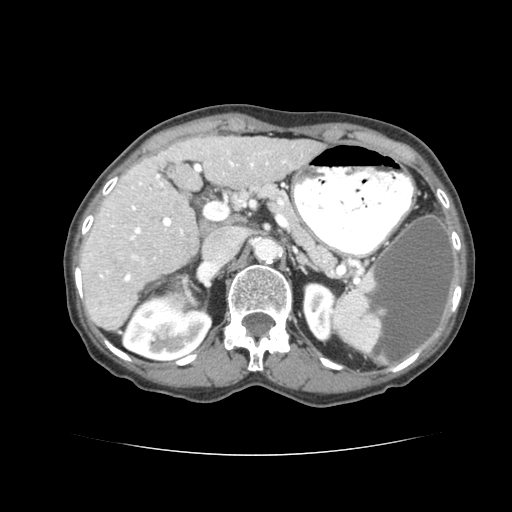
Contrast-enhanced abdominal CT (liver protocol), one axial slice; slice 42 of 77 in the series (ordered by position); soft-tissue window (W 400 / L 40 HU); 2.5 mm slice thickness; 512 × 512 image matrix. Case-level facts recorded for this patient, not image findings: diagnosis: hepatocellular carcinoma (patient treated with transarterial chemoembolisation; whether this scan precedes or follows treatment is not stated here); TNM stage (as recorded): Stage-I; Child-Pugh class: A; tumour differentiation: well differentiated; tumour size: 7.6 cm.
Annotated regions visible in this slice (semi-automatically segmented with operator editing):
- liver parenchyma outside the tumour (the mass and vessels are separate outlines, so this box may not span the whole liver): bounding box <78,138,320,330> (left, top, right, bottom; pixels)
- mass: <164,273,197,315>
- liver vessels: <105,161,270,276>